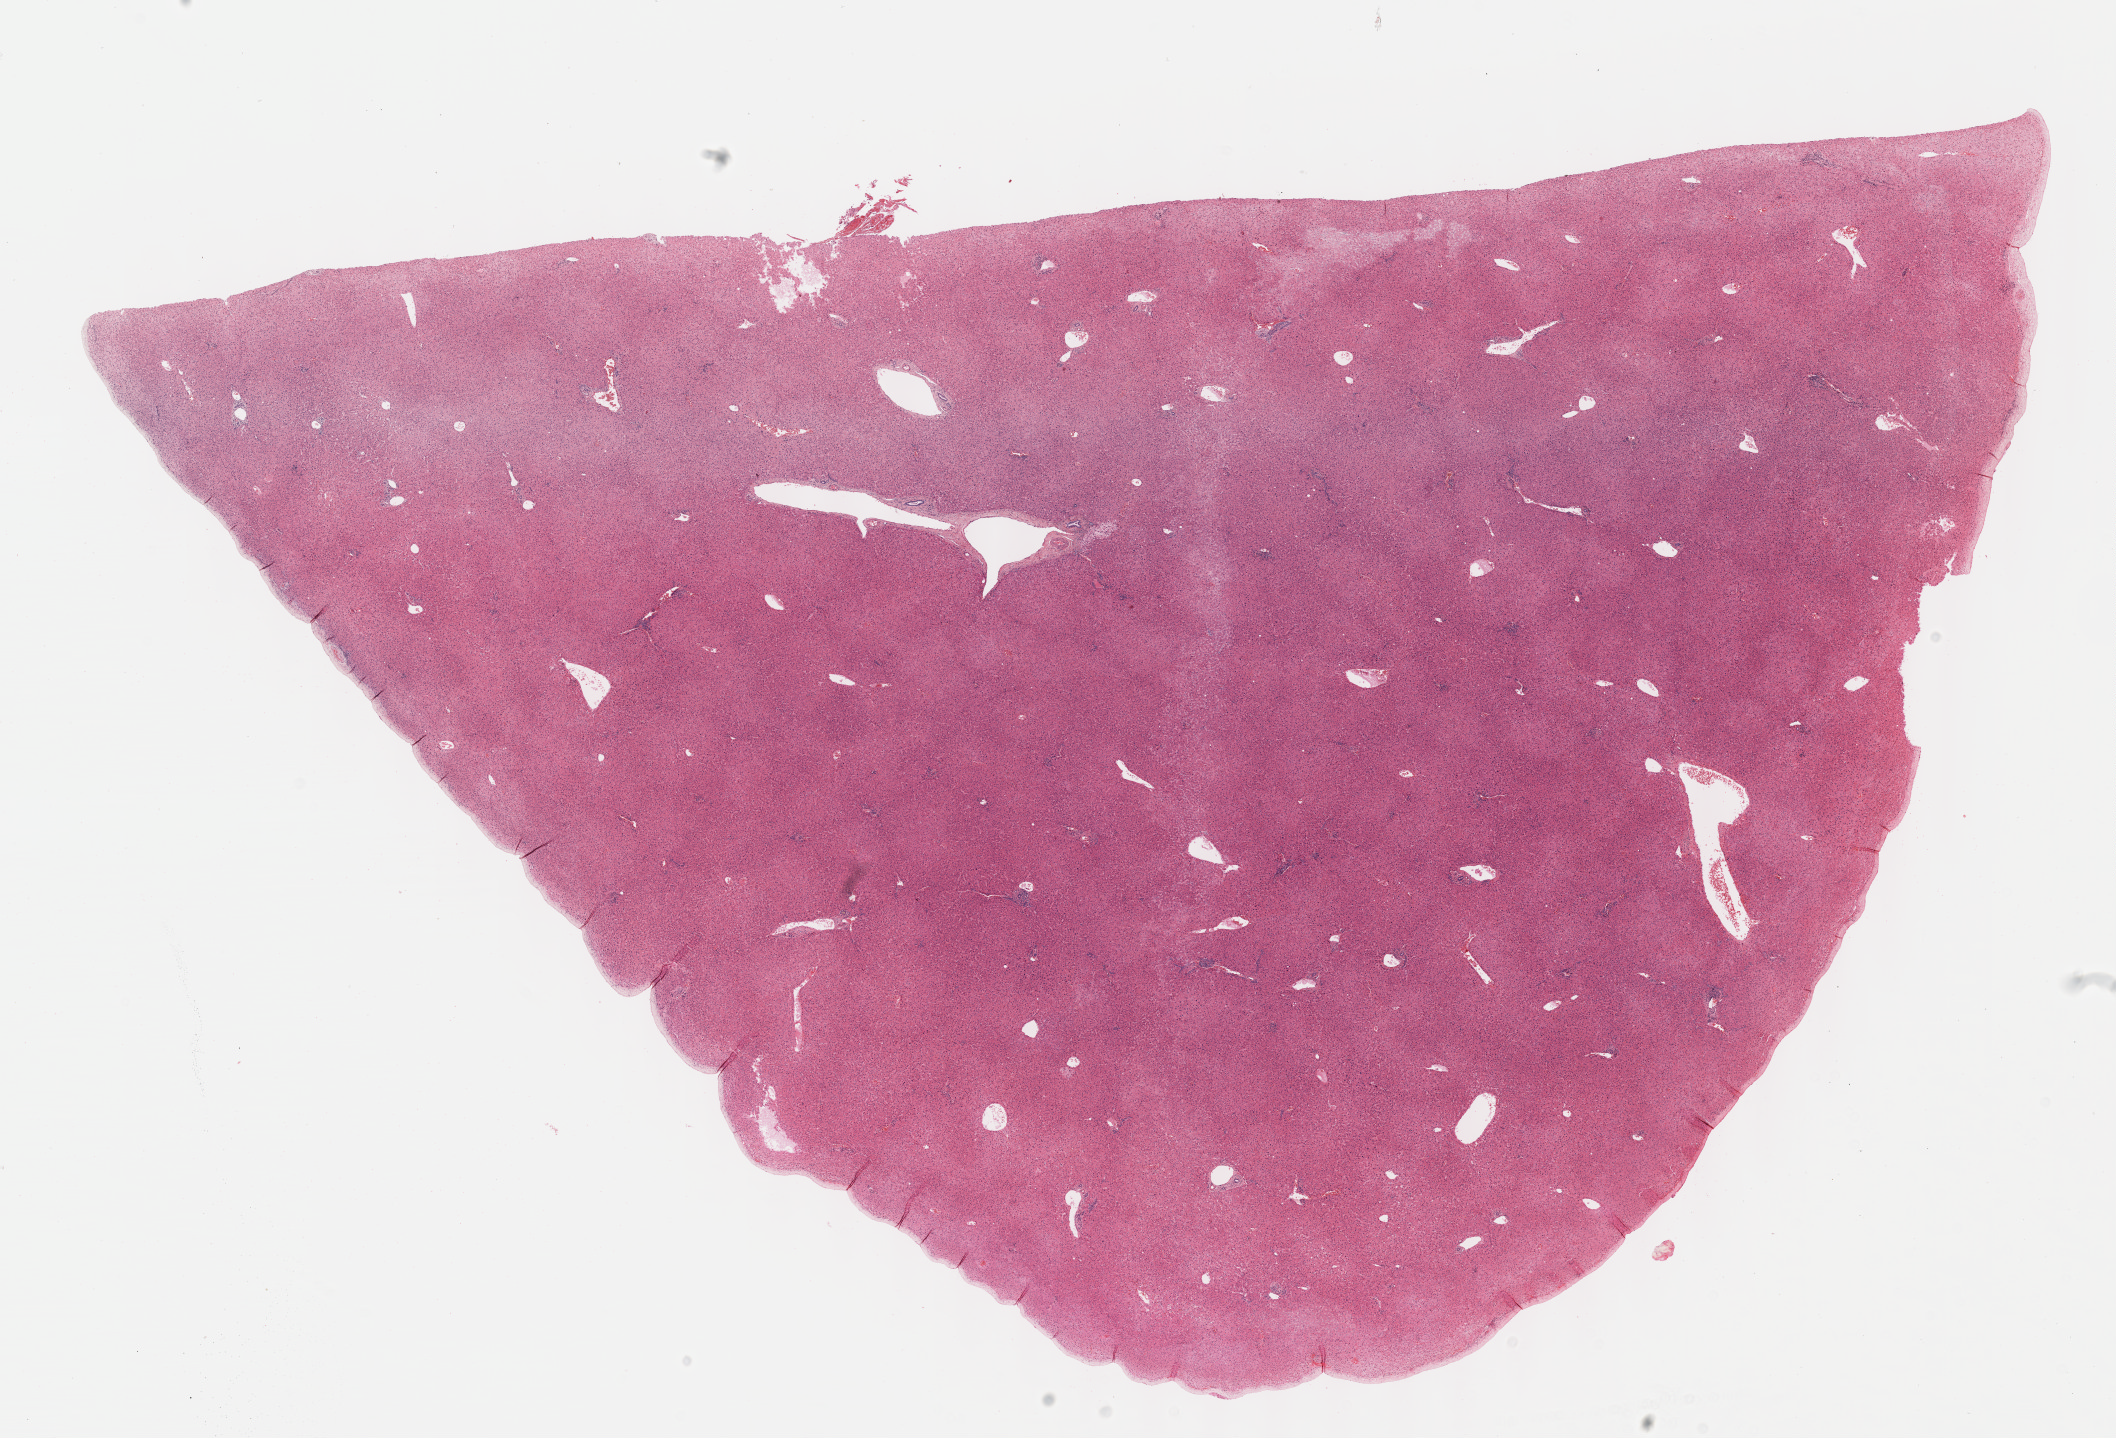
Whole-slide histology image, H&E-stained — a low-resolution overview of the entire scanned area, about 17.1 x 11.6 mm (acquisition: 40x scan). FFPE section. Primary tumour sample from the liver. Patient: male, age at initial diagnosis 70 years. Histologic grade: G2 (moderately differentiated).
* AJCC pathologic stage: I (7th edition)
* histologic diagnosis: Hepatocellular carcinoma, NOS
* TNM: T1 N0 M0